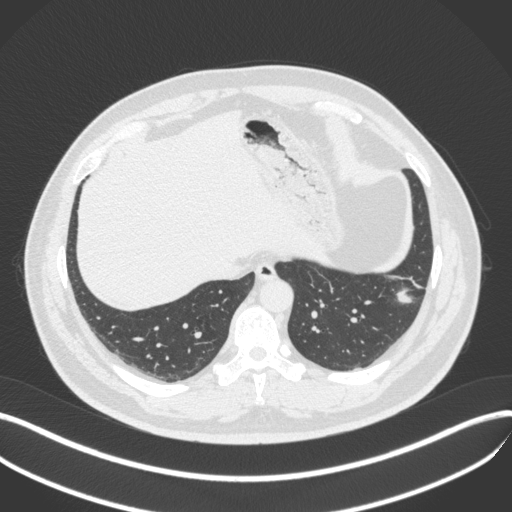
Chest CT, one axial slice; position 108 of 420 along the scan axis; lung window (W 1500 / L -600 HU); 1 mm slice thickness; 512 × 512 image matrix, field of view 400 × 400 mm. Male patient, age 39 years. Case-level facts recorded for this patient, not image findings: clinical TNM (as recorded): T2a N0 M0; histopathological grade: G2-3.
Structures marked on this image (bounding box drawn by a radiologist):
- lung tumour (recorded histology: adenocarcinoma): bounding box <391,282,415,307> (left, top, right, bottom; pixels)